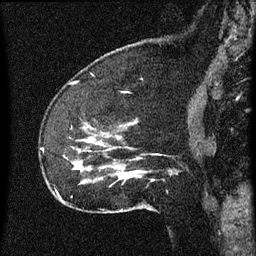
Breast MRI (dynamic contrast-enhanced), one sagittal slice. Slice 16 of 60 in the series (ordered by position). Dynamic contrast-enhanced series, image 2 of 3 at this slice position (ordered by acquisition). 1.5 T. TE 4.2 ms, TR 8 ms. 2 mm slice thickness. 256 × 256 image matrix, field of view 180 × 180 mm. Female patient, age 52 years.
Outlined on this slice (semi-automatically segmented with operator editing):
- analysis volume of interest (the breast-tissue region the enhancement analysis was run in; not a lesion): box from (x=54, y=122) to (x=162, y=207) px
- tumour enhancement mask (voxels above the 70 % enhancement threshold inside the analysis volume of interest): (x=77, y=138)–(x=143, y=175)